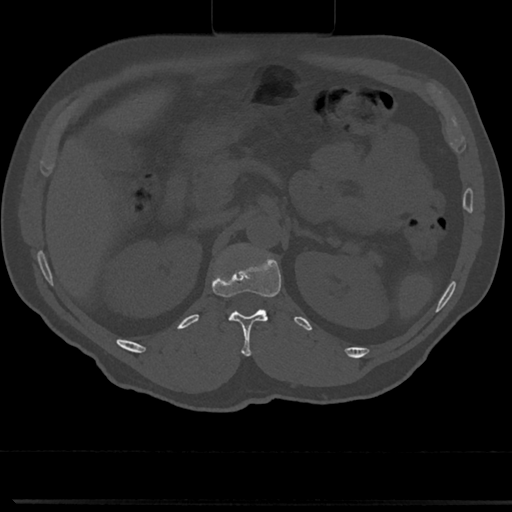
CT including the spine, one axial slice; position 129 of 817 along the scan axis; 120 kVp; bone window (W 1800 / L 400 HU); 512 × 512 image matrix, field of view 355 × 355 mm. Male patient, age 61 years. Case-level facts recorded for this patient, not image findings: primary cancer: prostate.
Structures marked on this image (semi-automatically segmented with operator editing):
- L1 vertebra: bounding box <219,243,255,315> (left, top, right, bottom; pixels)
- T12 vertebra: <226,269,282,357>